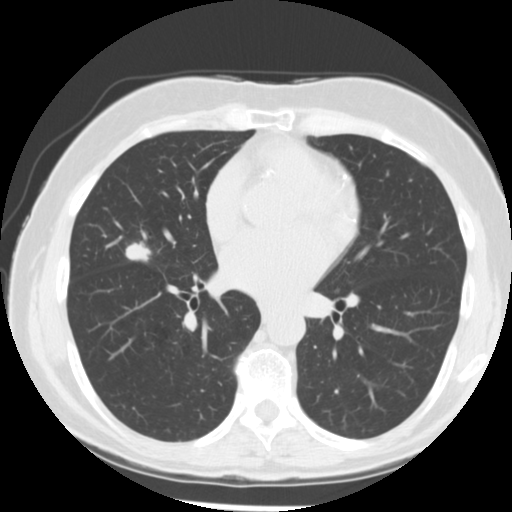
Low-dose screening chest CT, one axial slice. Reconstruction kernel STANDARD. 120 kVp. Lung window (W 1500 / L -600 HU). 512 × 512 image matrix, field of view 320 × 320 mm.
Structures marked on this image (manually delineated by an expert):
- lesion 1 (tumor, middle lobe of right lung): box from (x=125, y=242) to (x=151, y=262) px